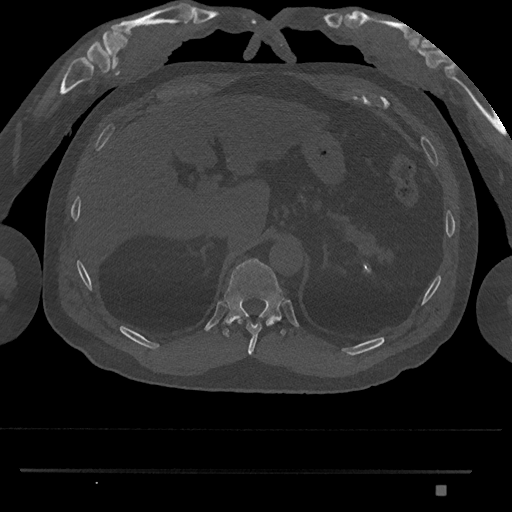
CT including the spine, one axial slice. Slice 968 of 1134 in the series (ordered by position). 120 kVp. Bone window (W 1800 / L 400 HU). 0.5 mm slice thickness. 512 × 512 image matrix, field of view 429 × 429 mm. Patient: male, 65 years. From the clinical record (not read from this slice): primary cancer: prostate.
Annotated regions visible in this slice (semi-automatic segmentation, software-assisted and operator-edited):
- T10 vertebra: box from (x=238, y=319) to (x=273, y=356) px
- T11 vertebra: (x=221, y=258)–(x=287, y=337)